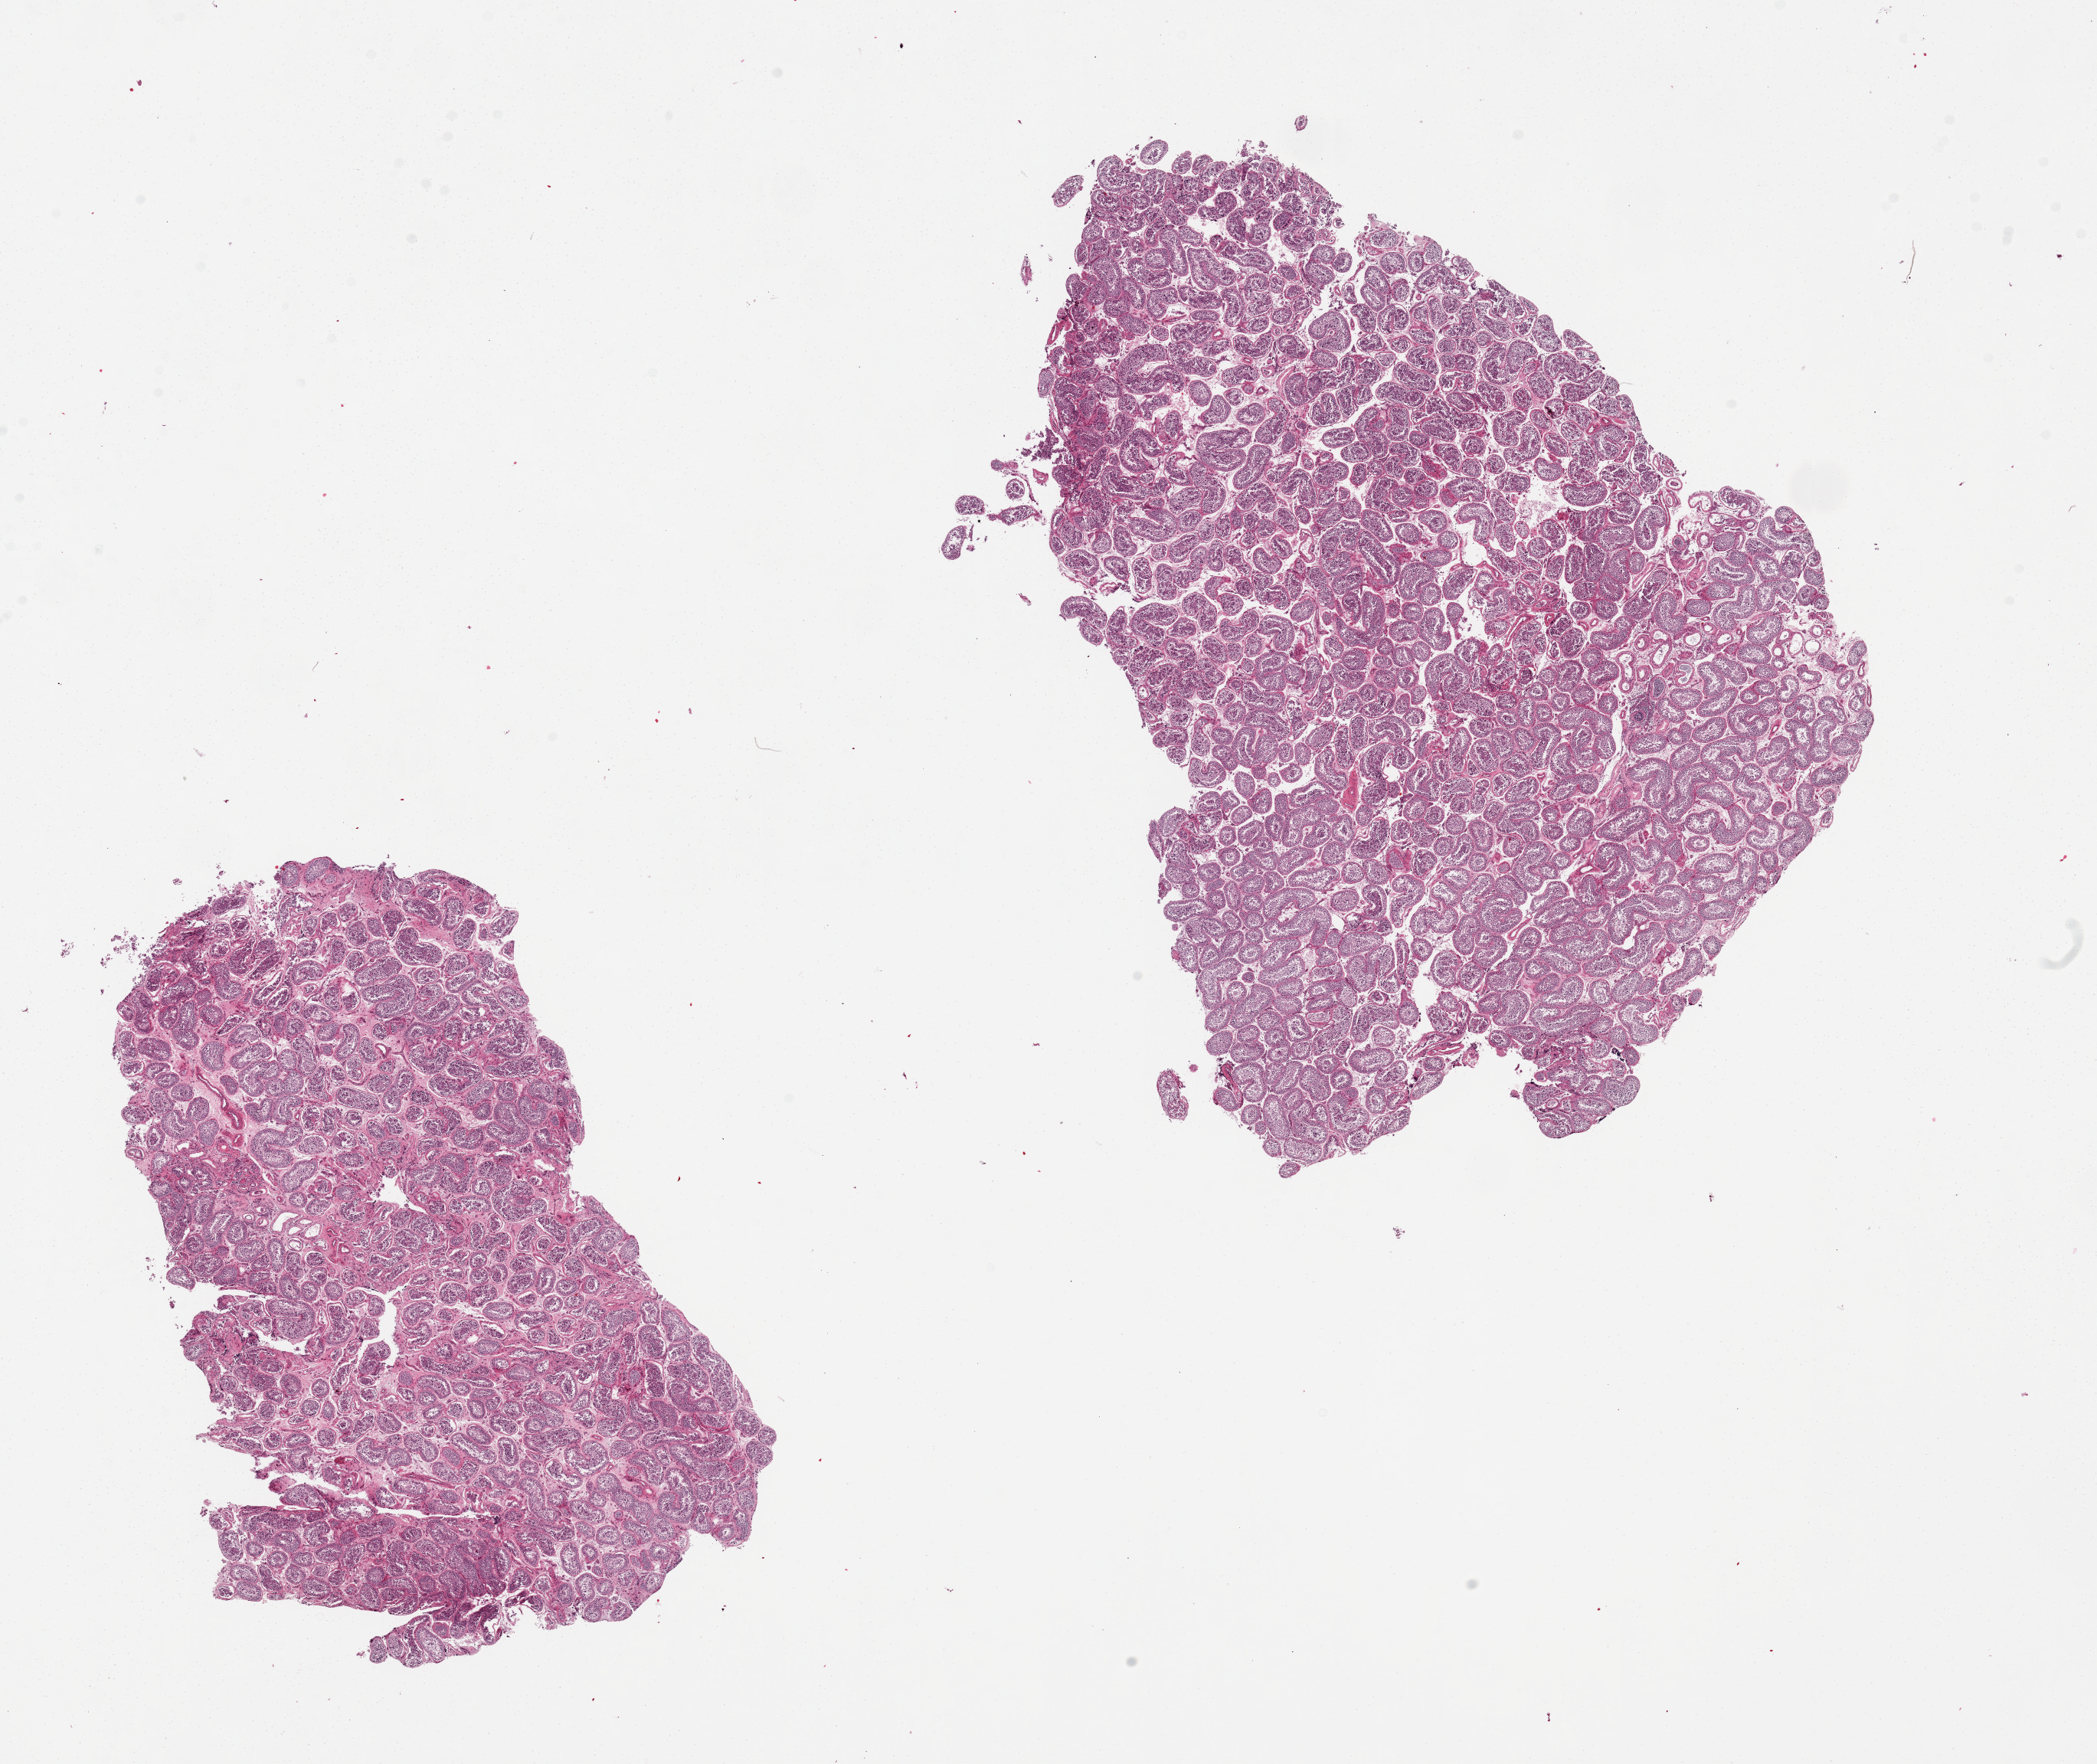
H&E whole-slide image, a low-resolution overview of the entire scanned area, about 21.7 x 18.2 mm. PAXgene-fixed paraffin-embedded (PFPE) section. Section of testis (target tissue). Tissue donor sample. Male donor.
Pathologist's review note for this sample: 2 pieces; active spermatogenesis.